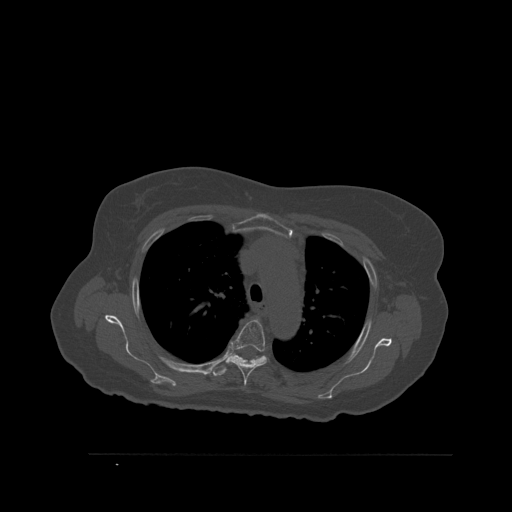
CT including the spine, one axial slice; slice 405 of 527 in the series (ordered by position); bone window (W 1800 / L 400 HU); 1.5 mm slice thickness; 512 × 512 image matrix. Female patient, age 73 years. Case-level facts recorded for this patient, not image findings: primary cancer: breast.
Annotated regions visible in this slice (semi-automatic segmentation, software-assisted and operator-edited):
- T4 vertebra: box from (x=226, y=320) to (x=269, y=387) px
- T5 vertebra: (x=210, y=354)–(x=269, y=377)